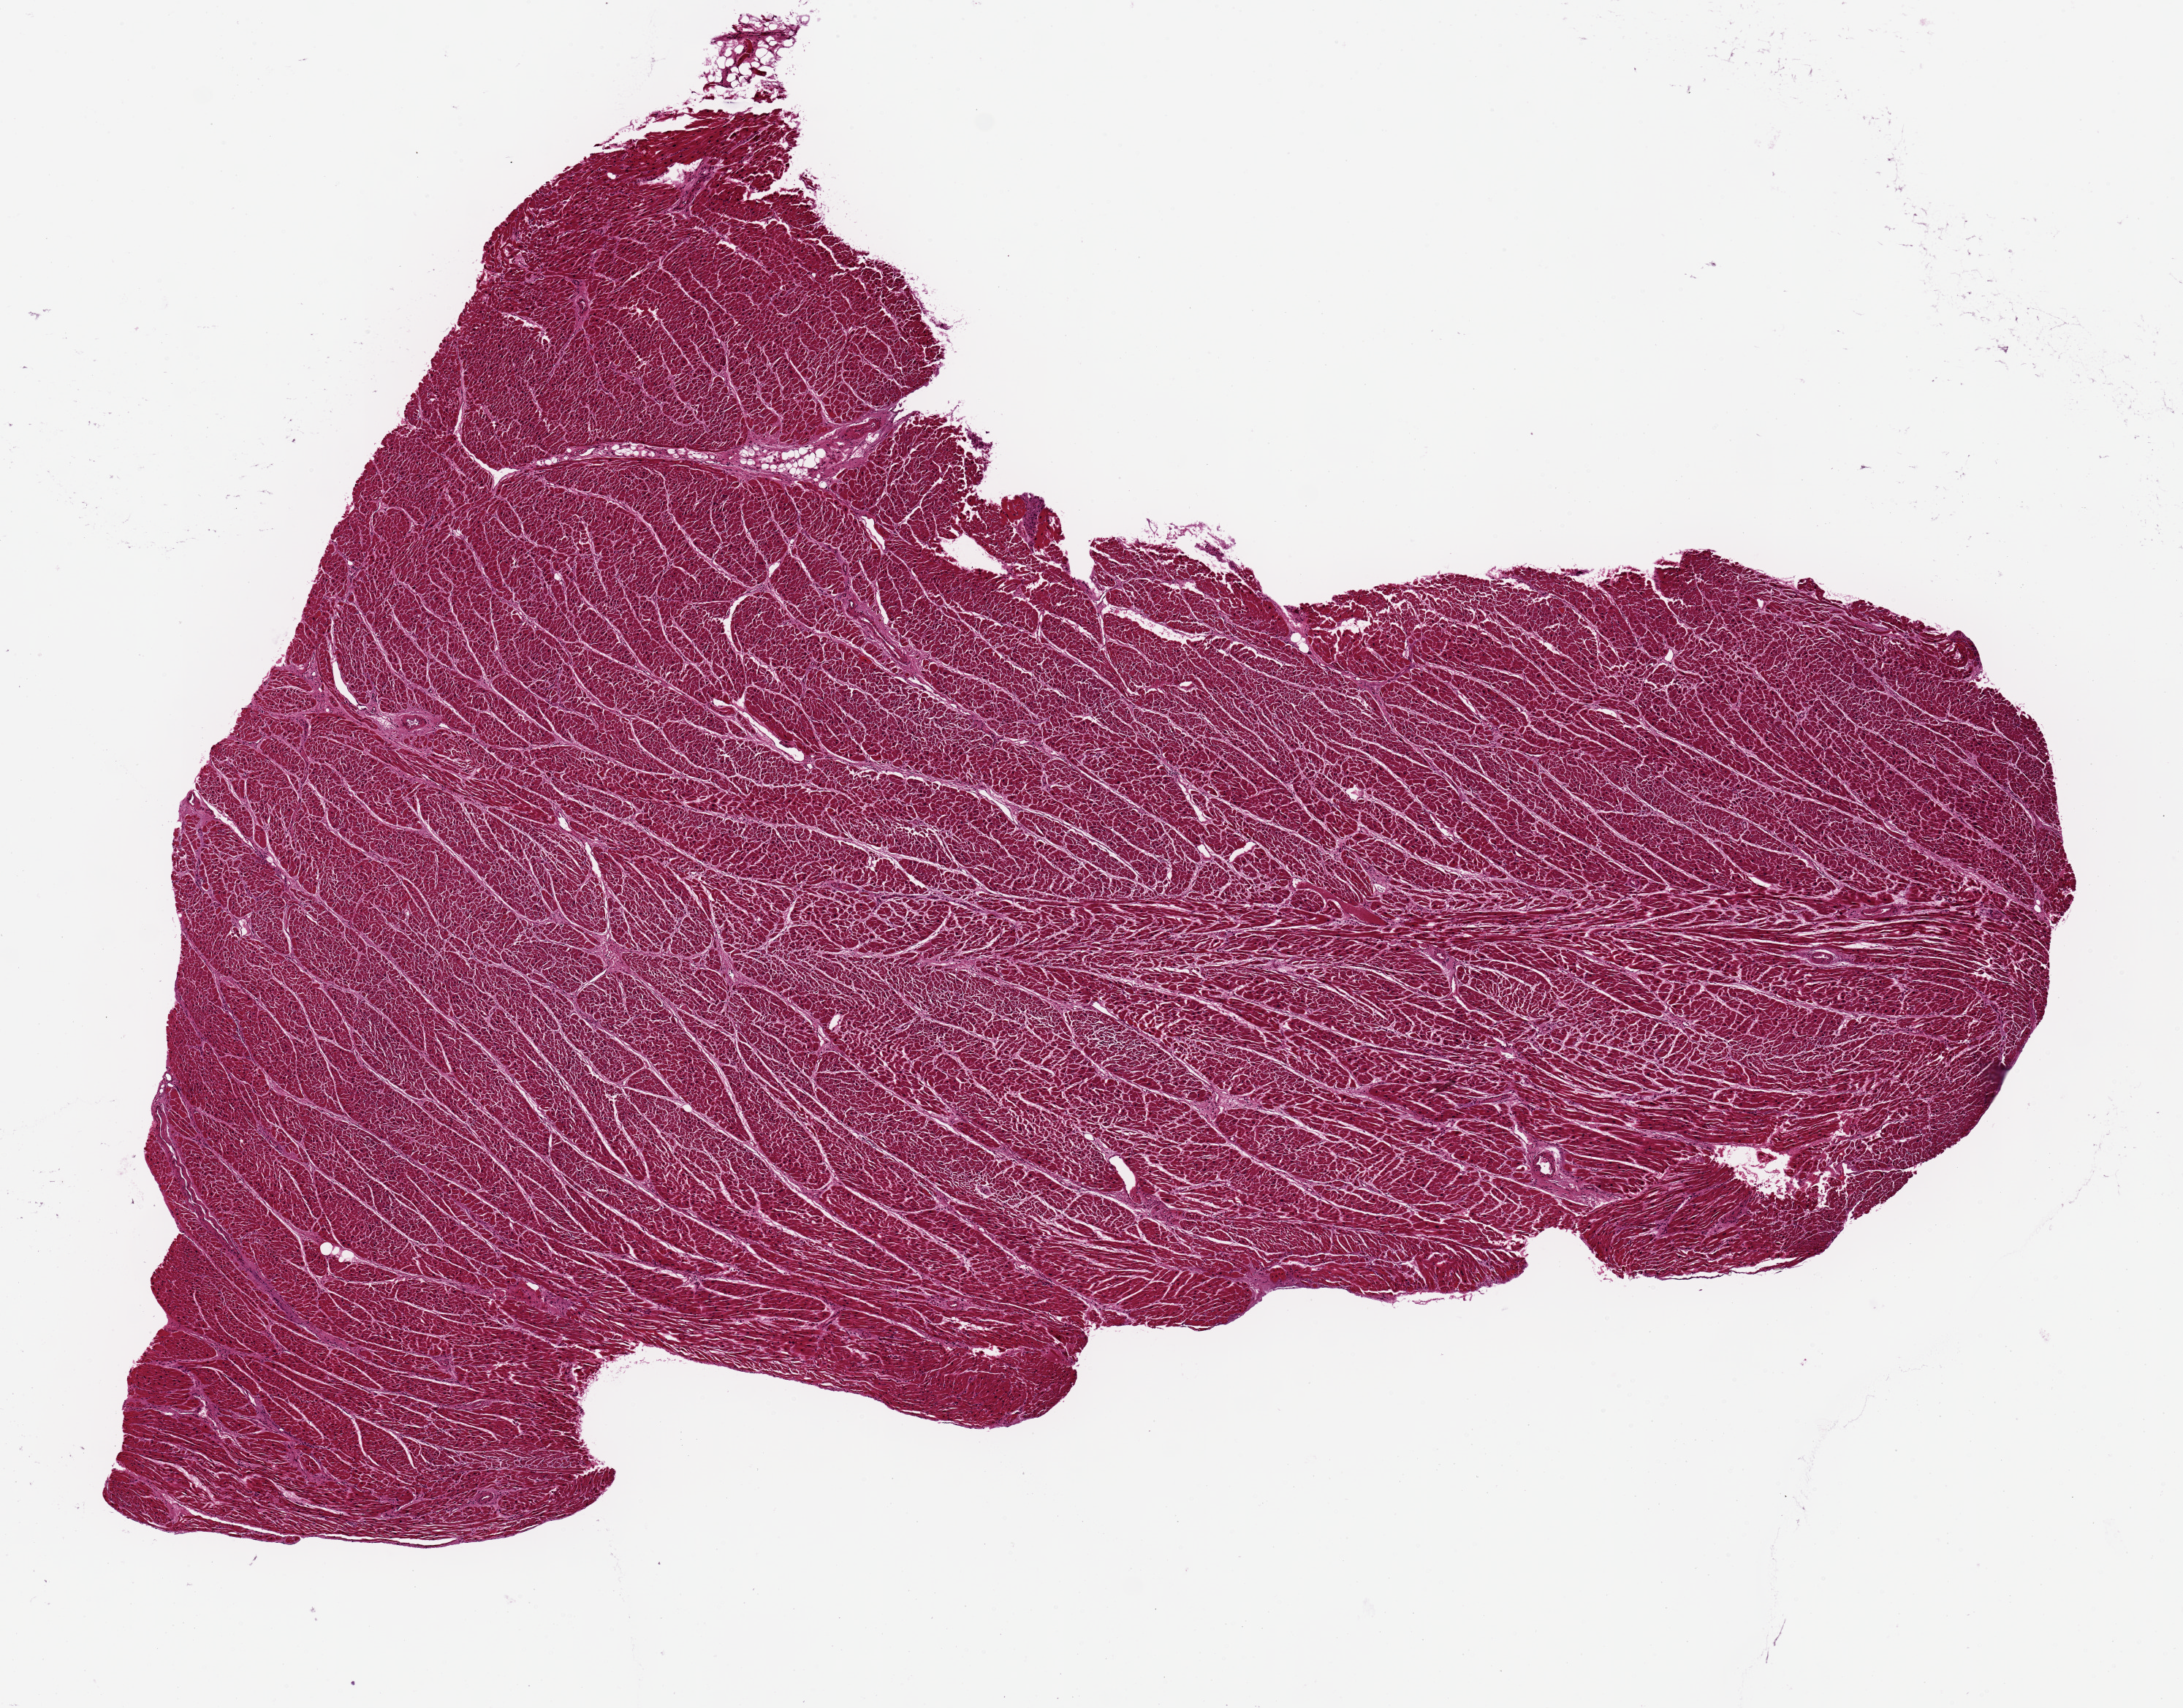
Digitized haematoxylin and eosin-stained section — a low-resolution overview of the entire scanned area, about 11.8 x 9.2 mm (acquisition: 20x scan); PAXgene-fixed, paraffin-embedded tissue; section of heart (target tissue); donor tissue sample. Donor sex: female.
Pathologist's review note for this sample: 10x8 mm.